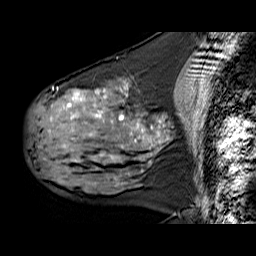
Breast MRI (dynamic contrast-enhanced), one sagittal slice; position 27 of 60 along the scan axis; dynamic contrast-enhanced series, time point 2 of 6 at this slice position (early post-contrast); 1.5 T; TE 6.3 ms, TR 32.9 ms; 256 × 256 image matrix, field of view 200 × 200 mm. Female patient. From the clinical record (not read from this slice): setting: breast cancer imaged before/during neoadjuvant chemotherapy; receptor status: HER2-positive.
Structures marked on this image (semi-automatic segmentation, software-assisted and operator-edited):
- analysis volume of interest (the breast-tissue region the enhancement analysis was run in; not a lesion): bounding box <30,78,169,180> (left, top, right, bottom; pixels)
- tumour enhancement mask (voxels above the 100 % enhancement threshold inside the analysis volume of interest): <67,83,154,158>